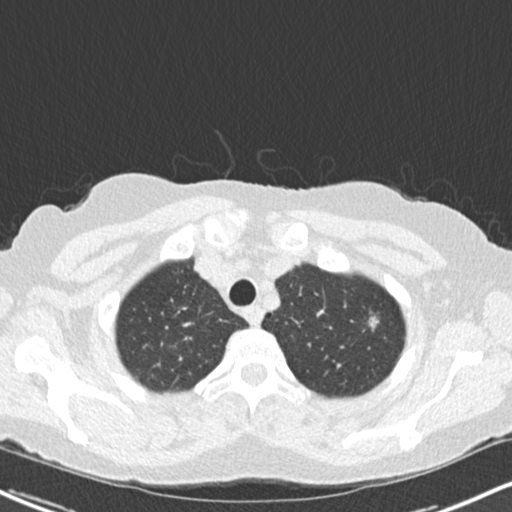
Chest CT (low-dose screening protocol), one axial image; first (baseline) screen; lung window (W 1500 / L -600 HU). Female, age 64 years at enrolment.
Lesion marked by an expert reader, bounding box [x1, y1, x2, y2] px = [358, 307, 388, 341]. The screening reader recorded 2 non-calcified nodules or masses ≥4 mm on this exam; which of them this box marks is not recorded. Lung cancer was diagnosed 477 days after this screen (after the second annual screen): signet ring cell carcinoma, right upper lobe, poorly differentiated (G3), stage IA (AJCC 6th edition), 15 mm at pathology.